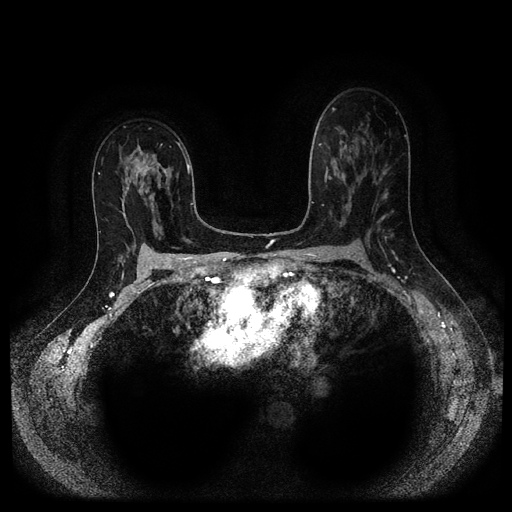
Breast MRI (dynamic contrast-enhanced, multi-phase), one axial slice. Slice 61 of 116 in the series (ordered by position). Dynamic contrast-enhanced series, time point 2 of 5 at this slice position (early post-contrast). 1.5 T. TE 2.6 ms, TR 5.3 ms. 2.2 mm slice thickness. 512 × 512 image matrix. Female patient, age 50 years.
Outlined on this slice (semi-automatically segmented with operator editing):
- breast lesion (labelled 'tumour' in the annotation; benign lesions carry a separate 'benign' label): bounding box [x1, y1, x2, y2] px = [129, 143, 161, 186]